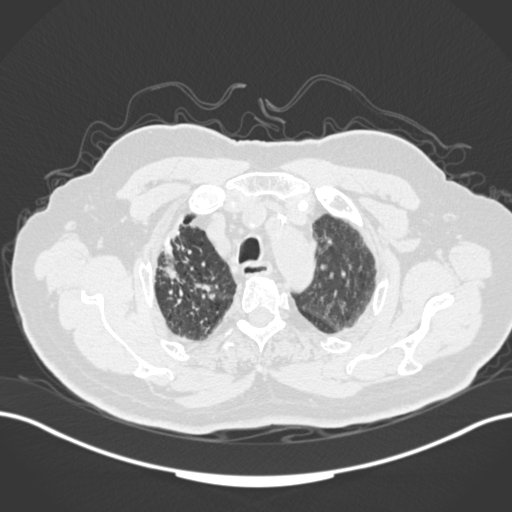
Chest CT, one axial slice. Slice 139 of 205 in the series (ordered by position). Reconstruction kernel B30f. Lung window (W 1500 / L -600 HU). 1 mm slice thickness. 512 × 512 image matrix, field of view 400 × 400 mm. Male patient, age 72 years. Case-level facts recorded for this patient, not image findings: clinical TNM (as recorded): T1a N0 M0.
Structures marked on this image (rectangle marked by the reading radiologist):
- lung tumour (recorded histology: squamous cell carcinoma): bounding box <160,220,190,285> (left, top, right, bottom; pixels)